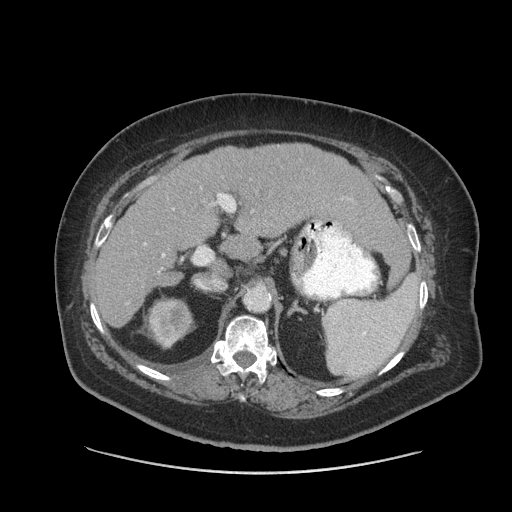
Contrast-enhanced abdominal CT (liver protocol), one axial slice. Reconstruction kernel STANDARD. 140 kVp. Soft-tissue window (W 400 / L 40 HU). 512 × 512 image matrix, field of view 420 × 420 mm. From the clinical record (not read from this slice): diagnosis: hepatocellular carcinoma (patient treated with transarterial chemoembolisation; whether this scan precedes or follows treatment is not stated here); TNM stage (as recorded): Stage-I; Child-Pugh class: A; tumour nodularity: uninodular.
Structures marked on this image (semi-automatically segmented with operator editing):
- liver parenchyma outside the tumour (the mass and vessels are separate outlines, so this box may not span the whole liver): box from (x=92, y=144) to (x=392, y=326) px
- liver vessels: (x=145, y=243)–(x=165, y=257)